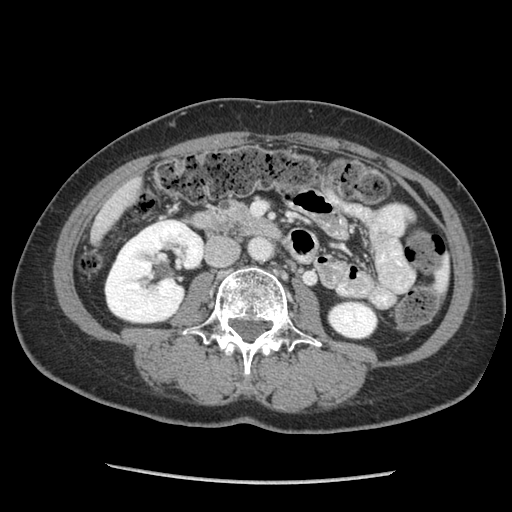
Contrast-enhanced abdominal CT (liver protocol), one axial slice; 140 kVp; soft-tissue window (W 400 / L 40 HU); 2.5 mm slice thickness; 512 × 512 image matrix. Case-level facts recorded for this patient, not image findings: diagnosis: hepatocellular carcinoma (patient treated with transarterial chemoembolisation; whether this scan precedes or follows treatment is not stated here); TNM stage (as recorded): Stage-I; Child-Pugh class: A; tumour nodularity: uninodular; tumour size: 11.1 cm.
Outlined on this slice (semi-automatic segmentation, software-assisted and operator-edited):
- liver parenchyma outside the tumour (the mass and vessels are separate outlines, so this box may not span the whole liver): box from (x=90, y=176) to (x=140, y=242) px